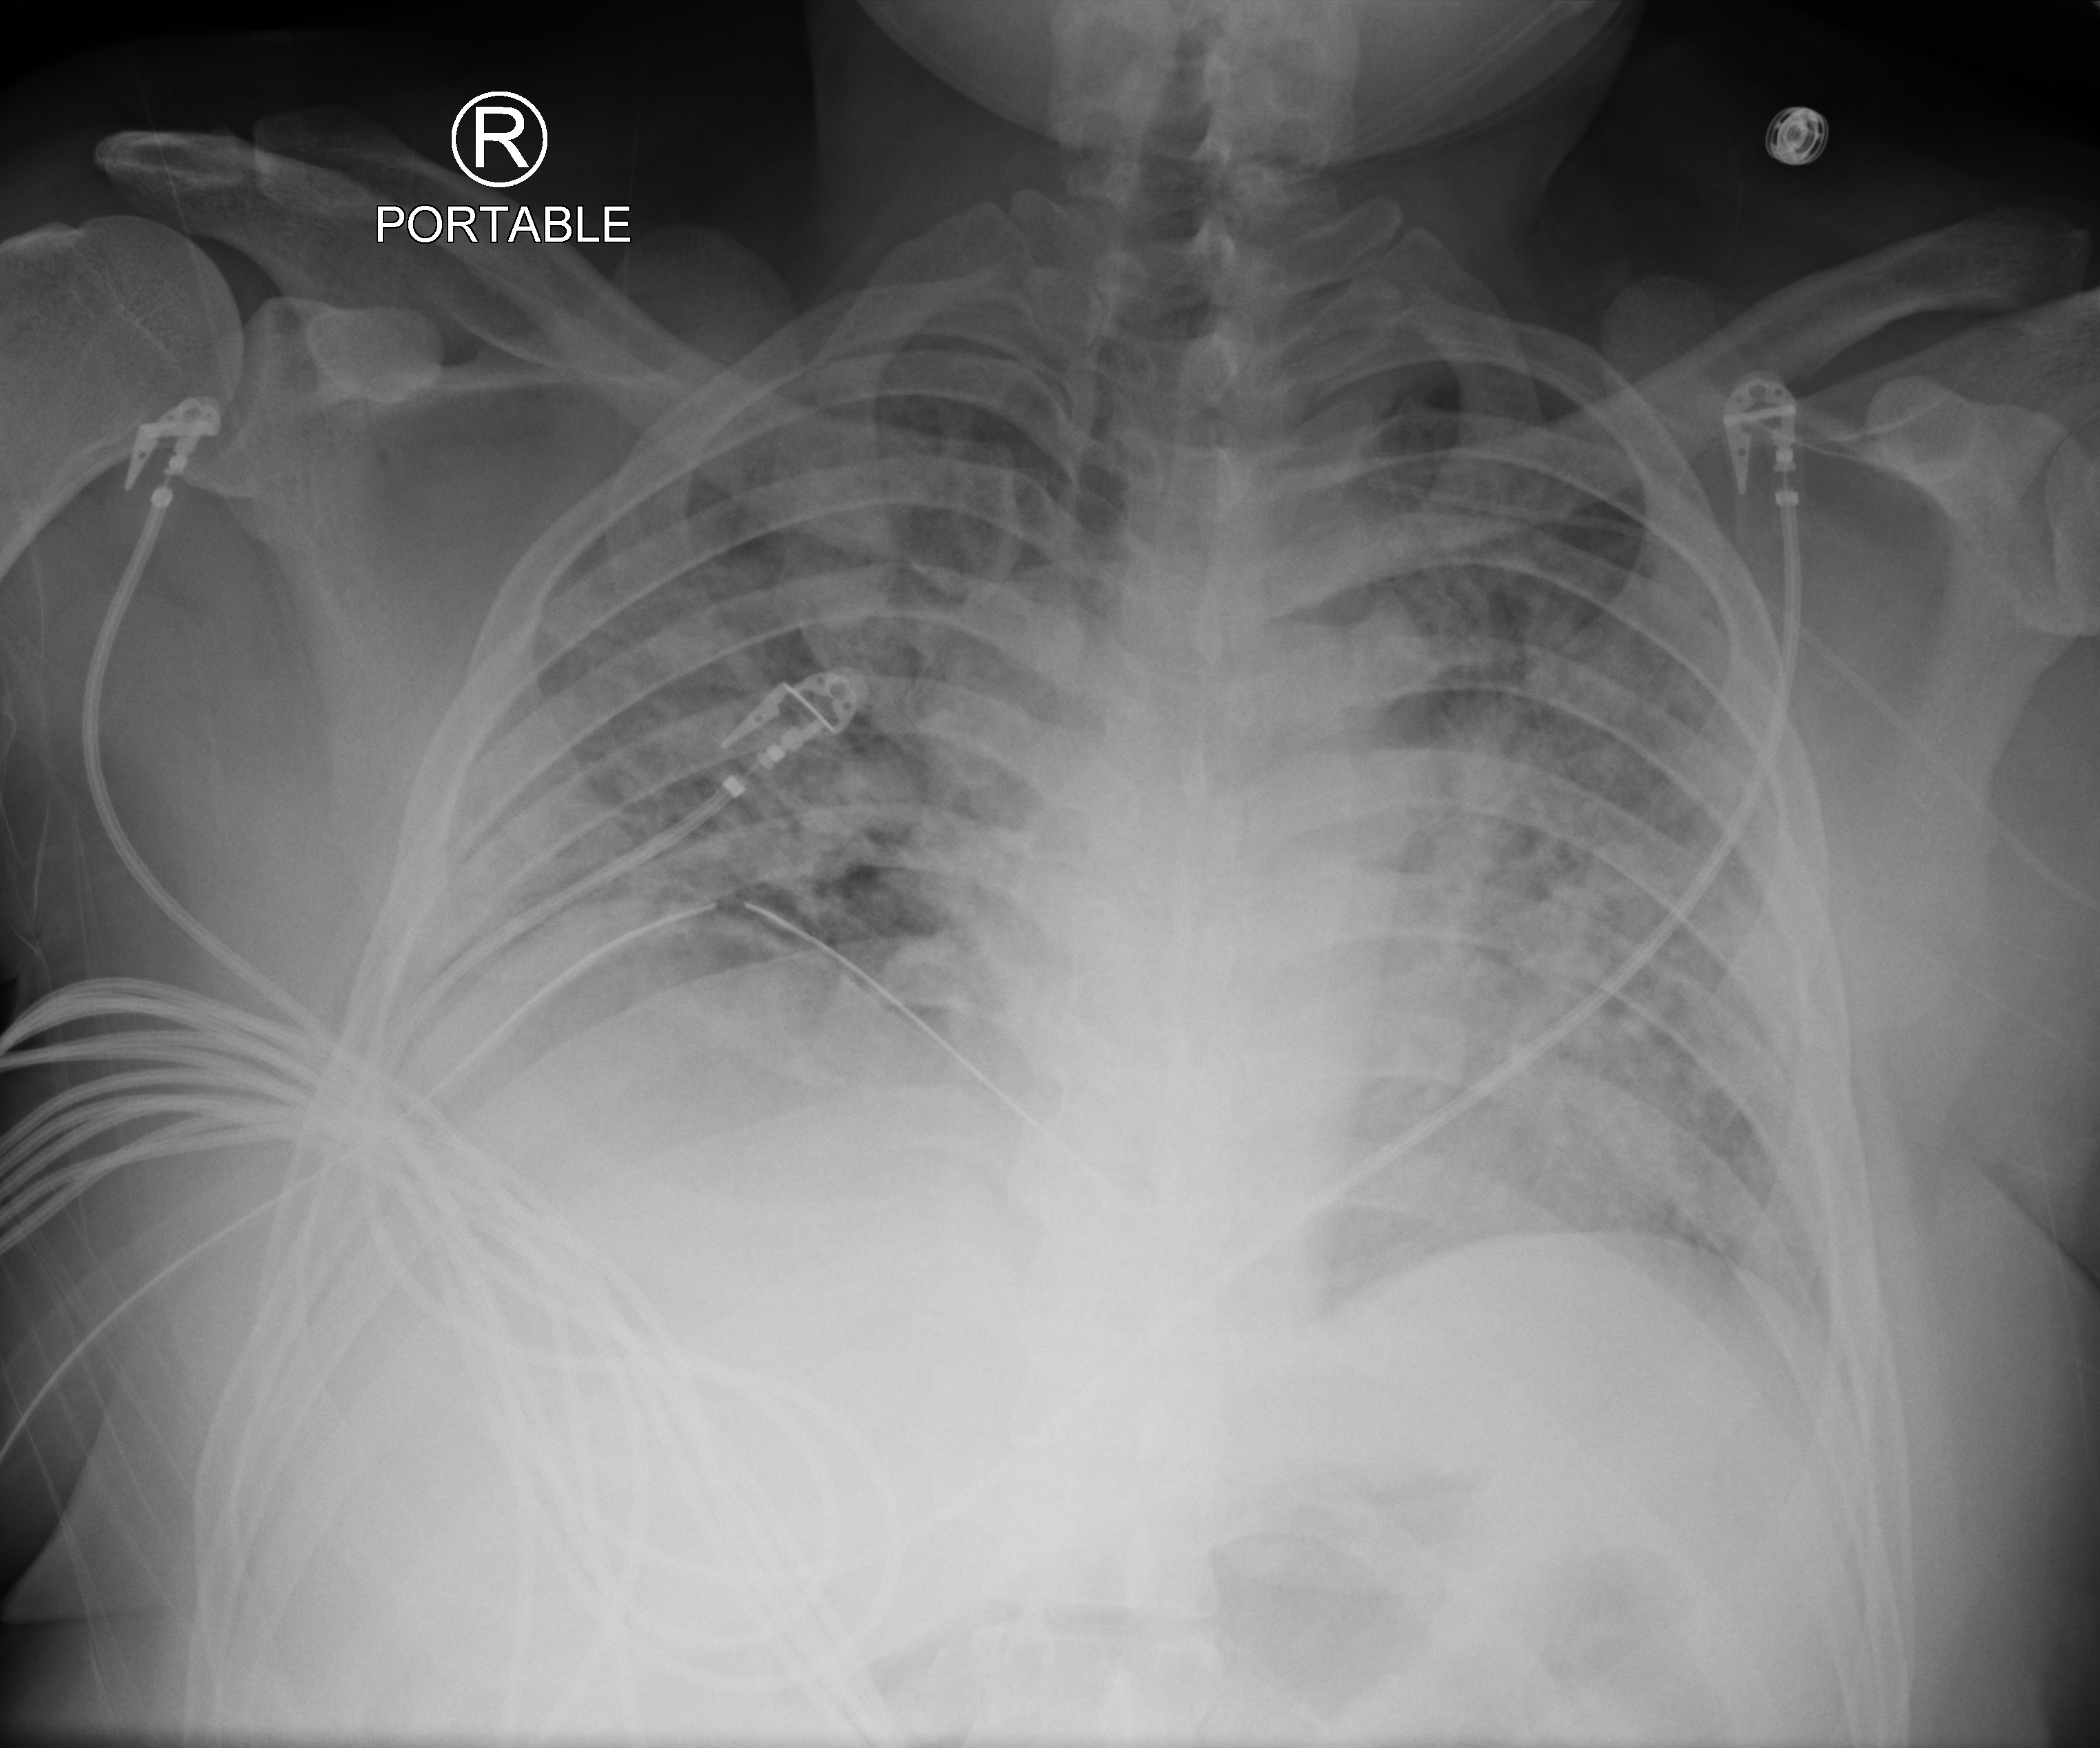
Bedside chest radiograph (computed radiography); anteroposterior (AP) projection. Male patient hospitalised with COVID-19, age 18–59 years.
From the hospital-stay record, not from the radiograph (when in the stay this image was taken is not recorded): mechanically ventilated during this hospital stay: yes.